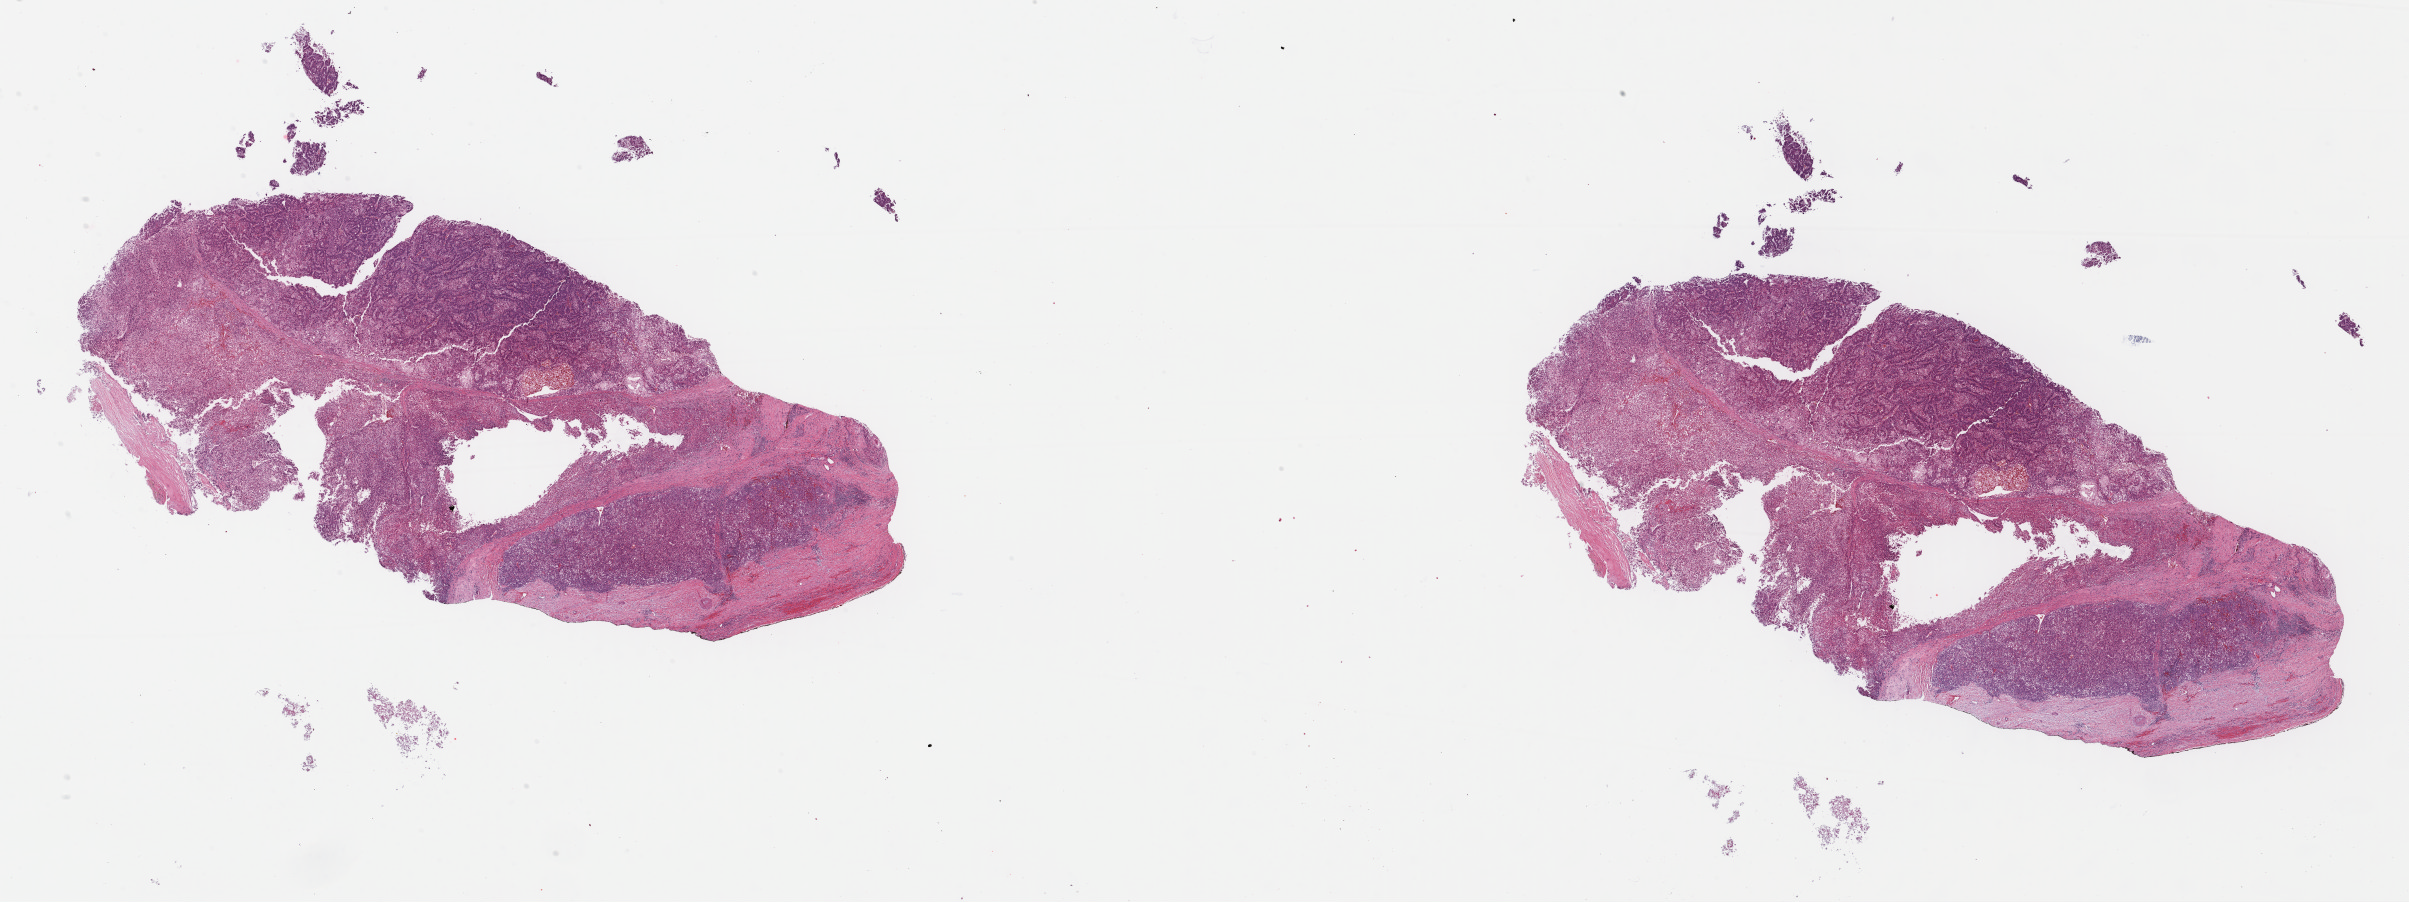
H&E whole-slide image — shown as a low-resolution overview of the whole scanned area (about 37.9 x 14.2 mm, slide scanned at 40x), formalin-fixed paraffin-embedded (FFPE) diagnostic section, liver, primary tumour sample. Patient: female, age at initial diagnosis 46 years. Histologic grade: G2 (moderately differentiated).
AJCC pathologic stage: I (7th edition). Histologic diagnosis: Hepatocellular carcinoma, NOS.